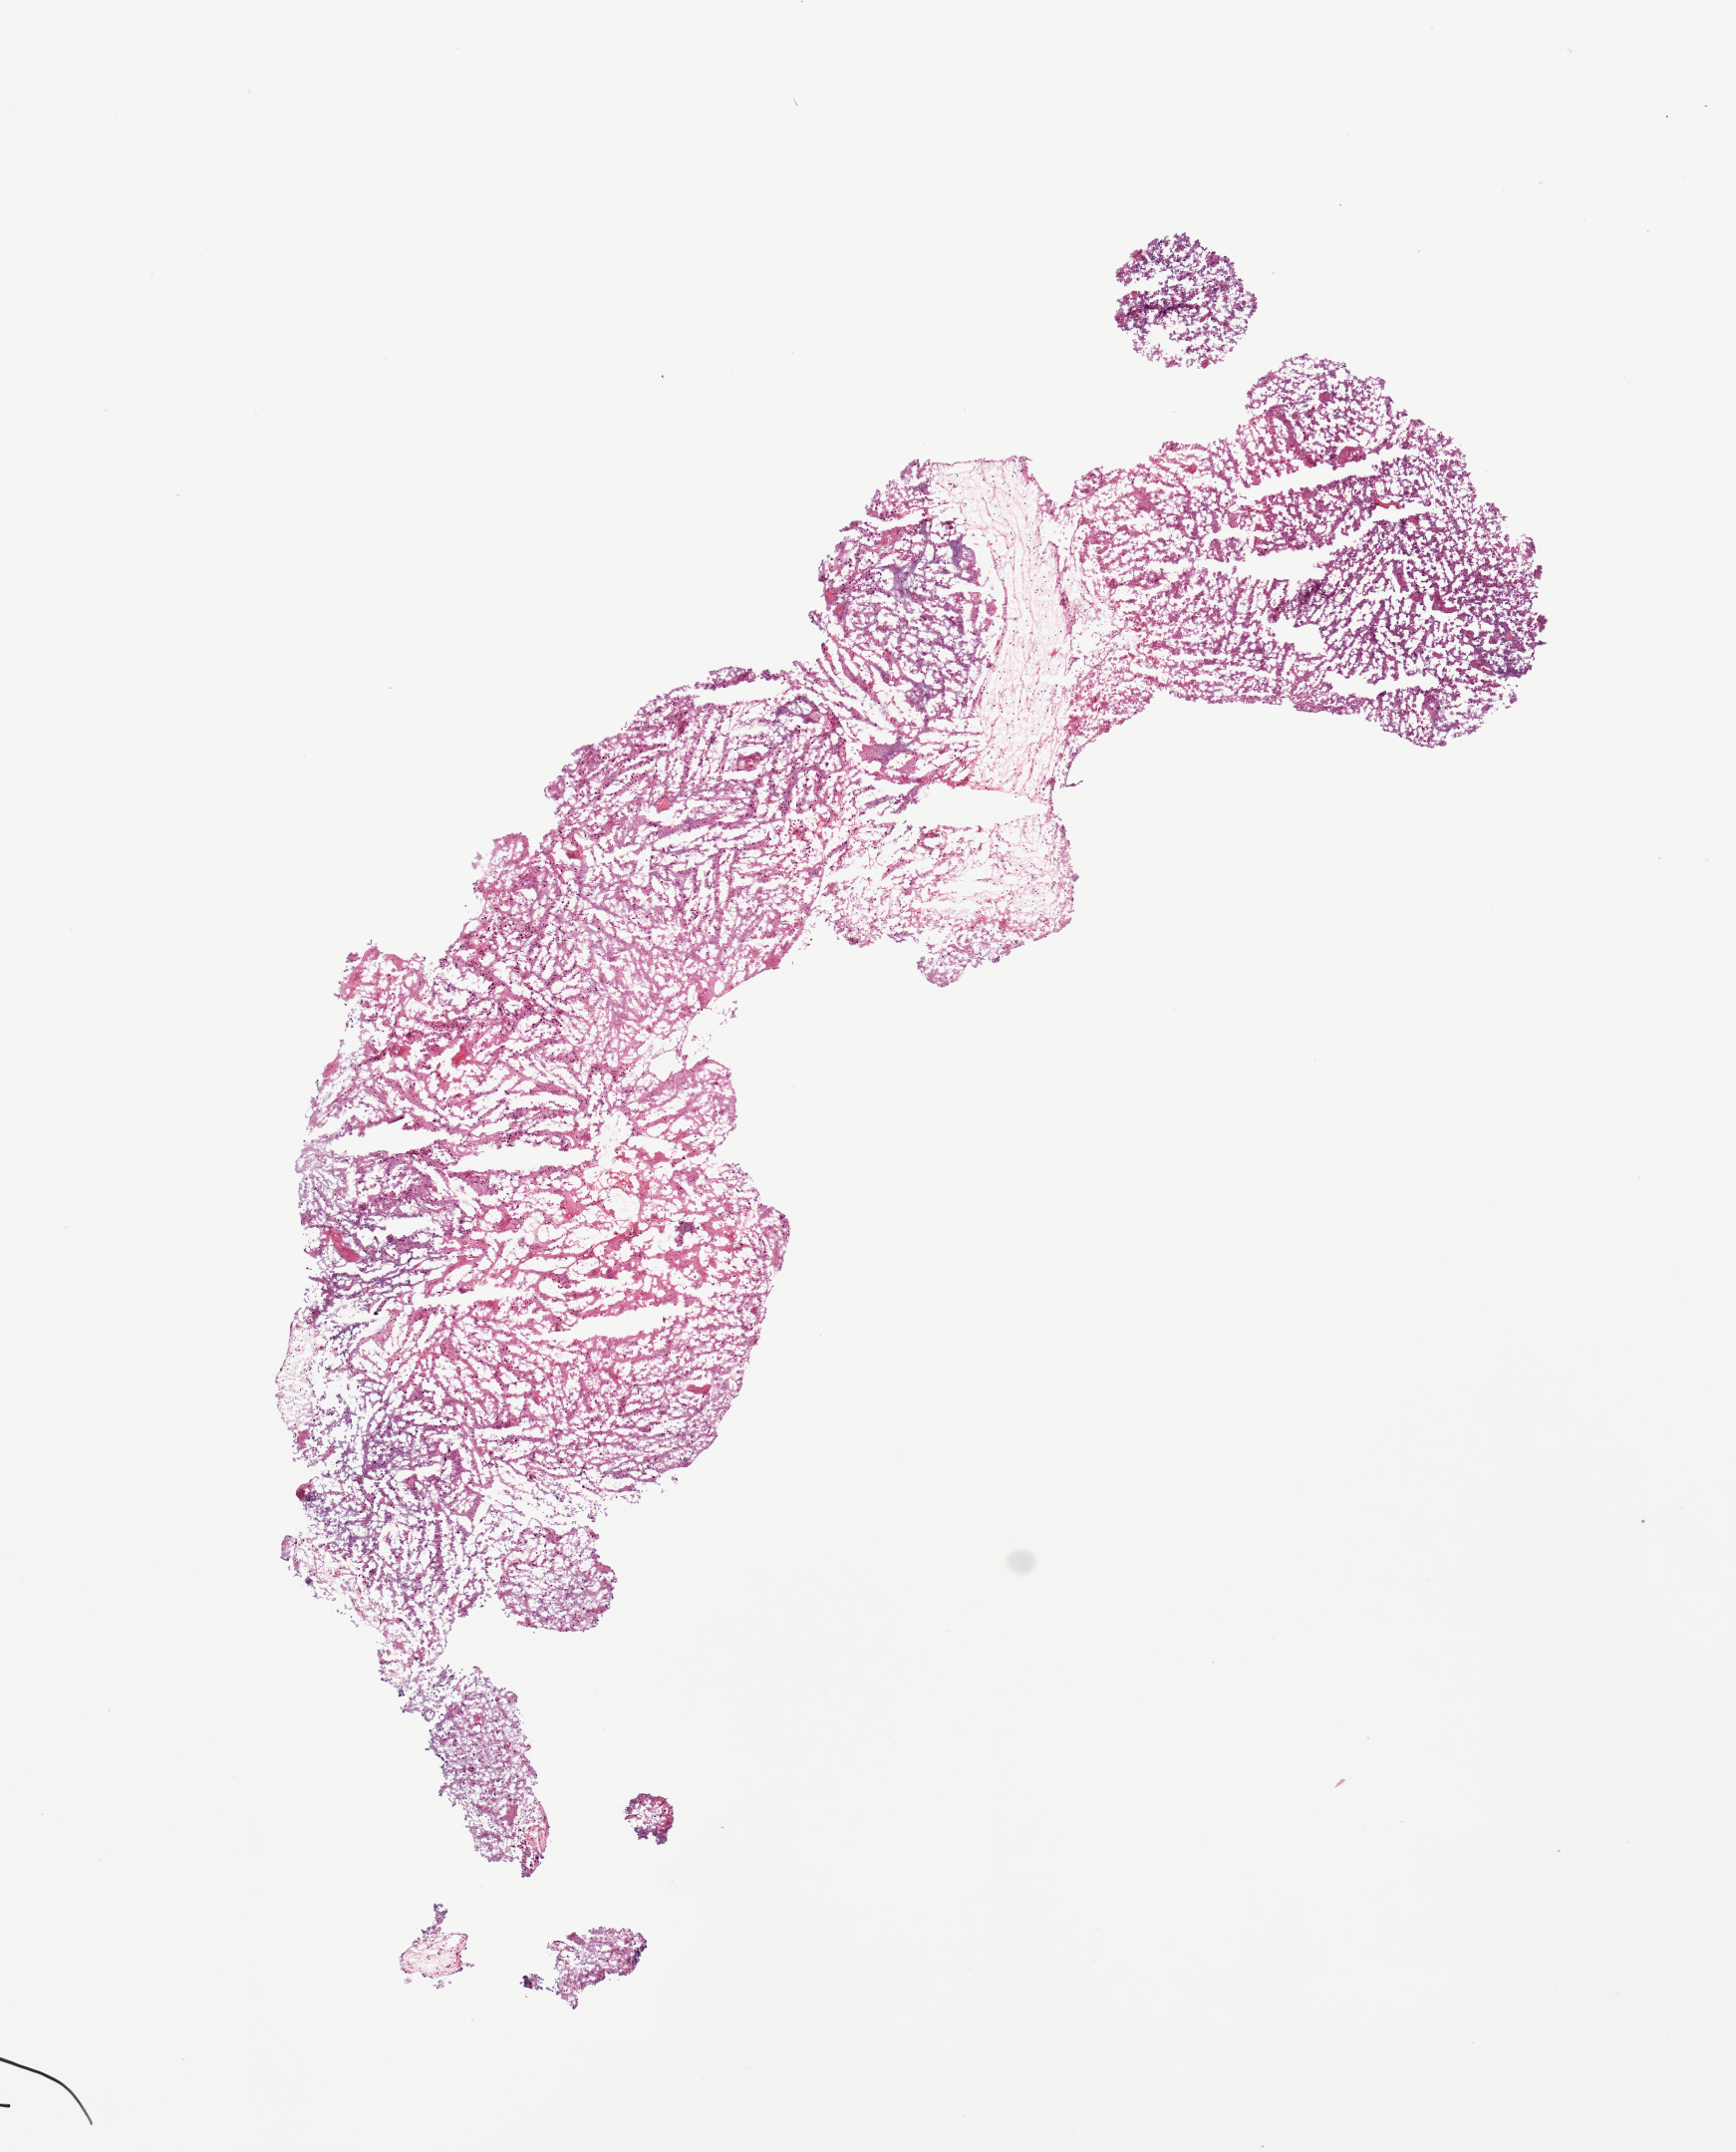
Whole-slide histology image, H&E, shown as a low-resolution overview of the whole scanned area (about 6.9 x 8.5 mm, from a 20x scan); brain, tumour tissue. Patient: female, age 74 years.
• primary tumour site (as recorded): temporal lobe
• patient diagnosis (cohort enrolment): glioblastoma multiforme (brain)